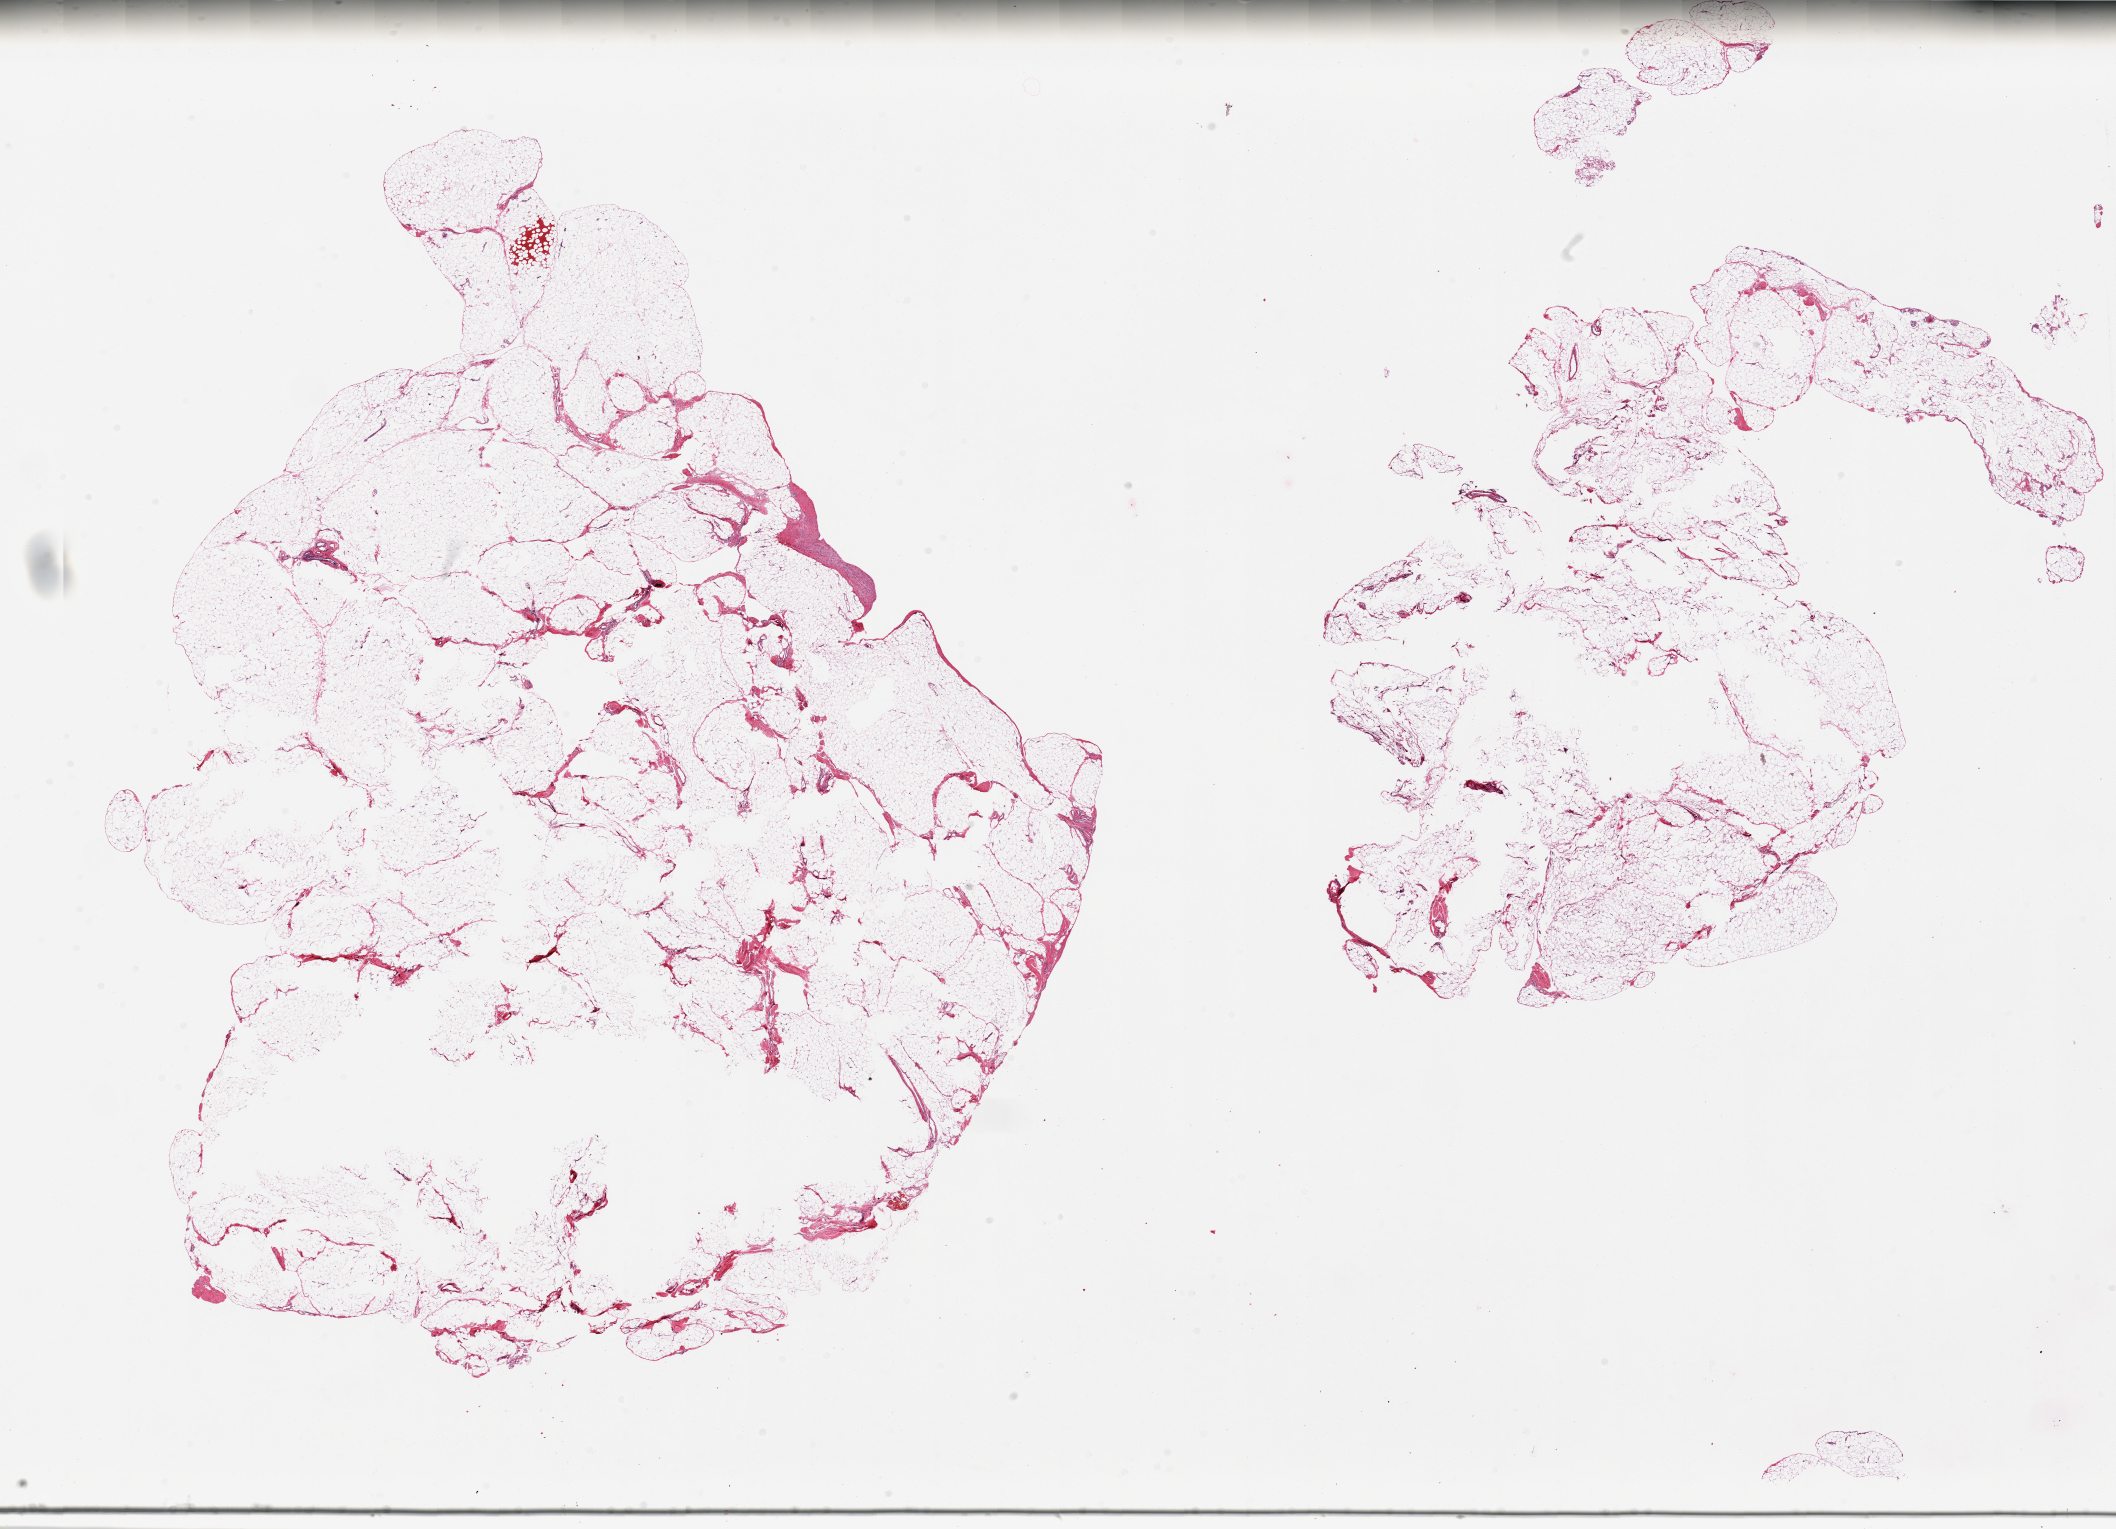
Whole-slide image, hematoxylin and eosin (H&E) stain, shown as a low-resolution overview of the whole scanned area (about 33.5 x 24.2 mm). PAXgene-fixed paraffin-embedded (PFPE) section. Target tissue: omentum. Tissue donor sample. Donor sex: female.
Review note (as recorded): 2 pieces; large pieces with interior holes.